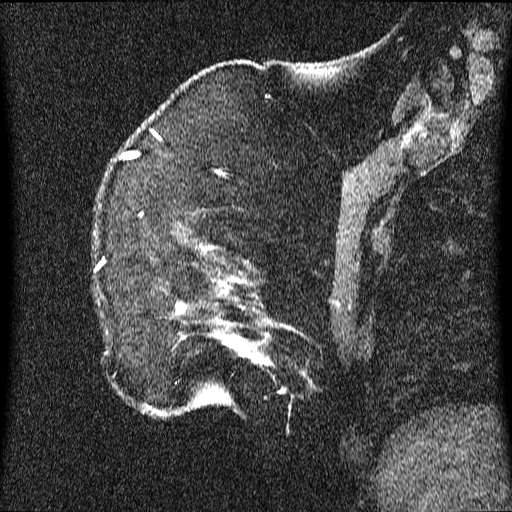
Breast MRI (dynamic contrast-enhanced), one sagittal slice; slice 12 of 64 in the series (ordered by position); dynamic contrast-enhanced series, image 2 of 3 at this slice position (ordered by acquisition); 1.5 T; TE 4.2 ms, TR 9.1 ms; 2.2 mm slice thickness; 512 × 512 image matrix, field of view 180 × 180 mm. Patient: female, 52 years.
Structures marked on this image (semi-automatic segmentation, software-assisted and operator-edited):
- analysis volume of interest (the breast-tissue region the enhancement analysis was run in; not a lesion): bounding box <95,203,350,417> (left, top, right, bottom; pixels)
- tumour enhancement mask (voxels above the 70 % enhancement threshold inside the analysis volume of interest): <158,305,269,415>